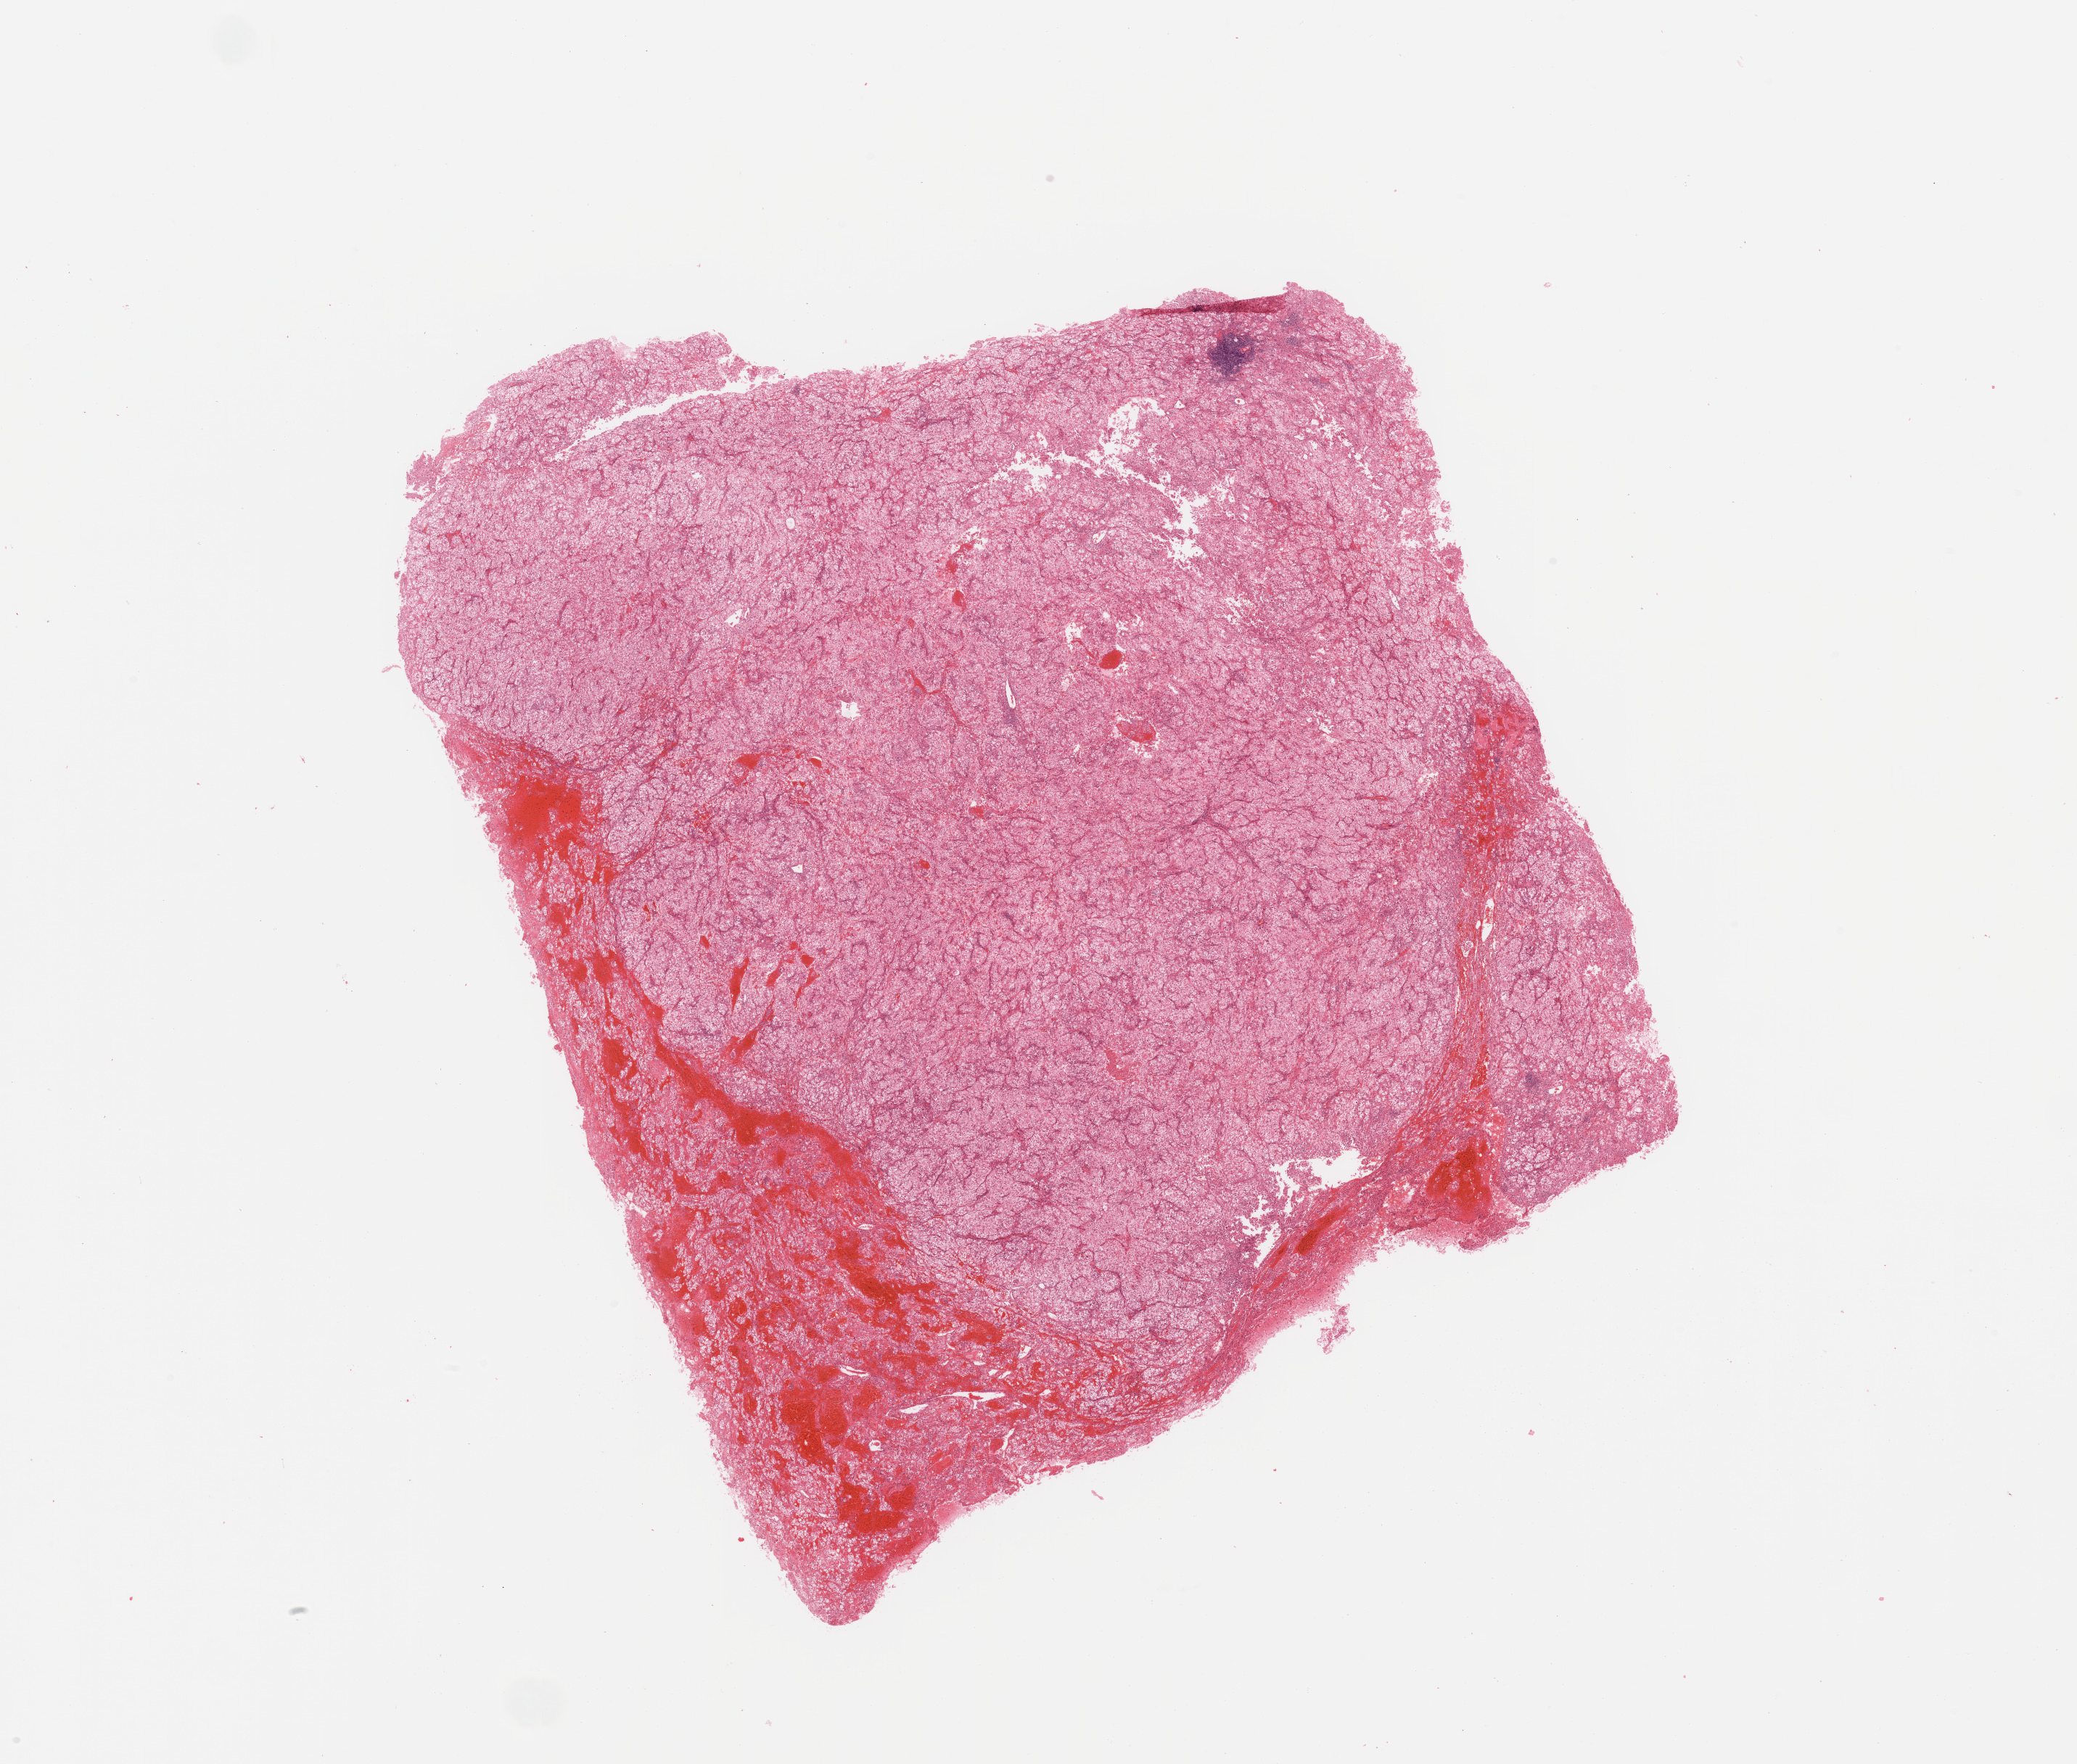
Whole-slide histology image, H&E — low-resolution overview of the scanned area, about 22.6 x 19.2 mm, kidney, tumour tissue. Patient: male, age 68 years. Histologic grade: G3 (poorly differentiated).
- AJCC pathologic stage: II
- histologic diagnosis: Renal cell carcinoma, NOS